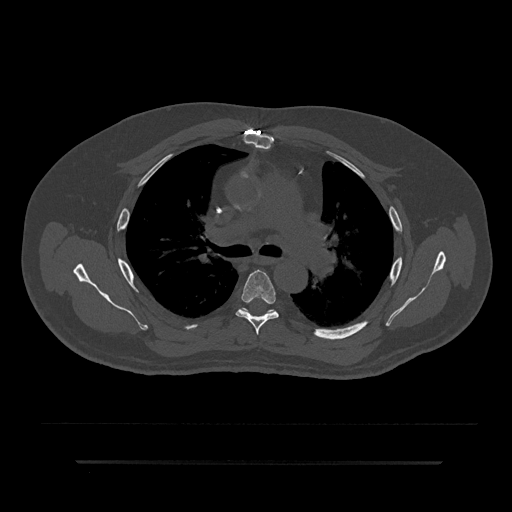
CT including the spine, one axial slice; slice 568 of 797 in the series (ordered by position); 120 kVp; bone window (W 1800 / L 400 HU); 512 × 512 image matrix. Male patient, age 59 years. From the clinical record (not read from this slice): primary cancer: bile ducts.
Annotated regions visible in this slice (semi-automatic segmentation, software-assisted and operator-edited):
- T5 vertebra: bounding box (x1, y1, x2, y2) in pixels: (235, 270, 279, 335)
- T6 vertebra: (241, 308, 271, 313)